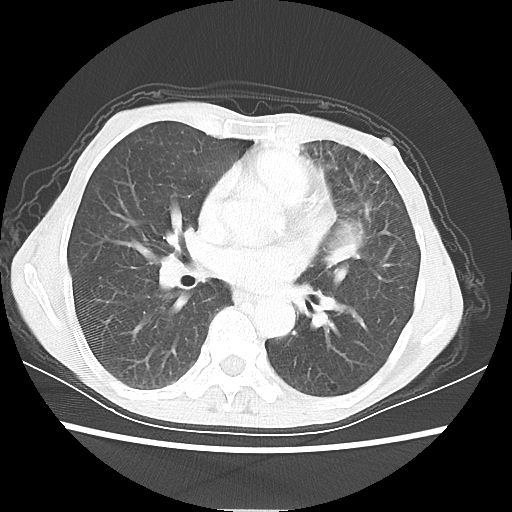
Chest CT, one axial slice. Slice 30 of 56 in the series (ordered by position). 80 kVp. Lung window (W 1500 / L -600 HU). 512 × 512 image matrix, field of view 331 × 331 mm. Patient: female, 60 years. Case-level facts recorded for this patient, not image findings: clinical TNM (as recorded): T4 N1 M0.
Annotated regions visible in this slice (rectangle marked by the reading radiologist):
- lung tumour (recorded histology: adenocarcinoma): bounding box <325,222,362,283> (left, top, right, bottom; pixels)